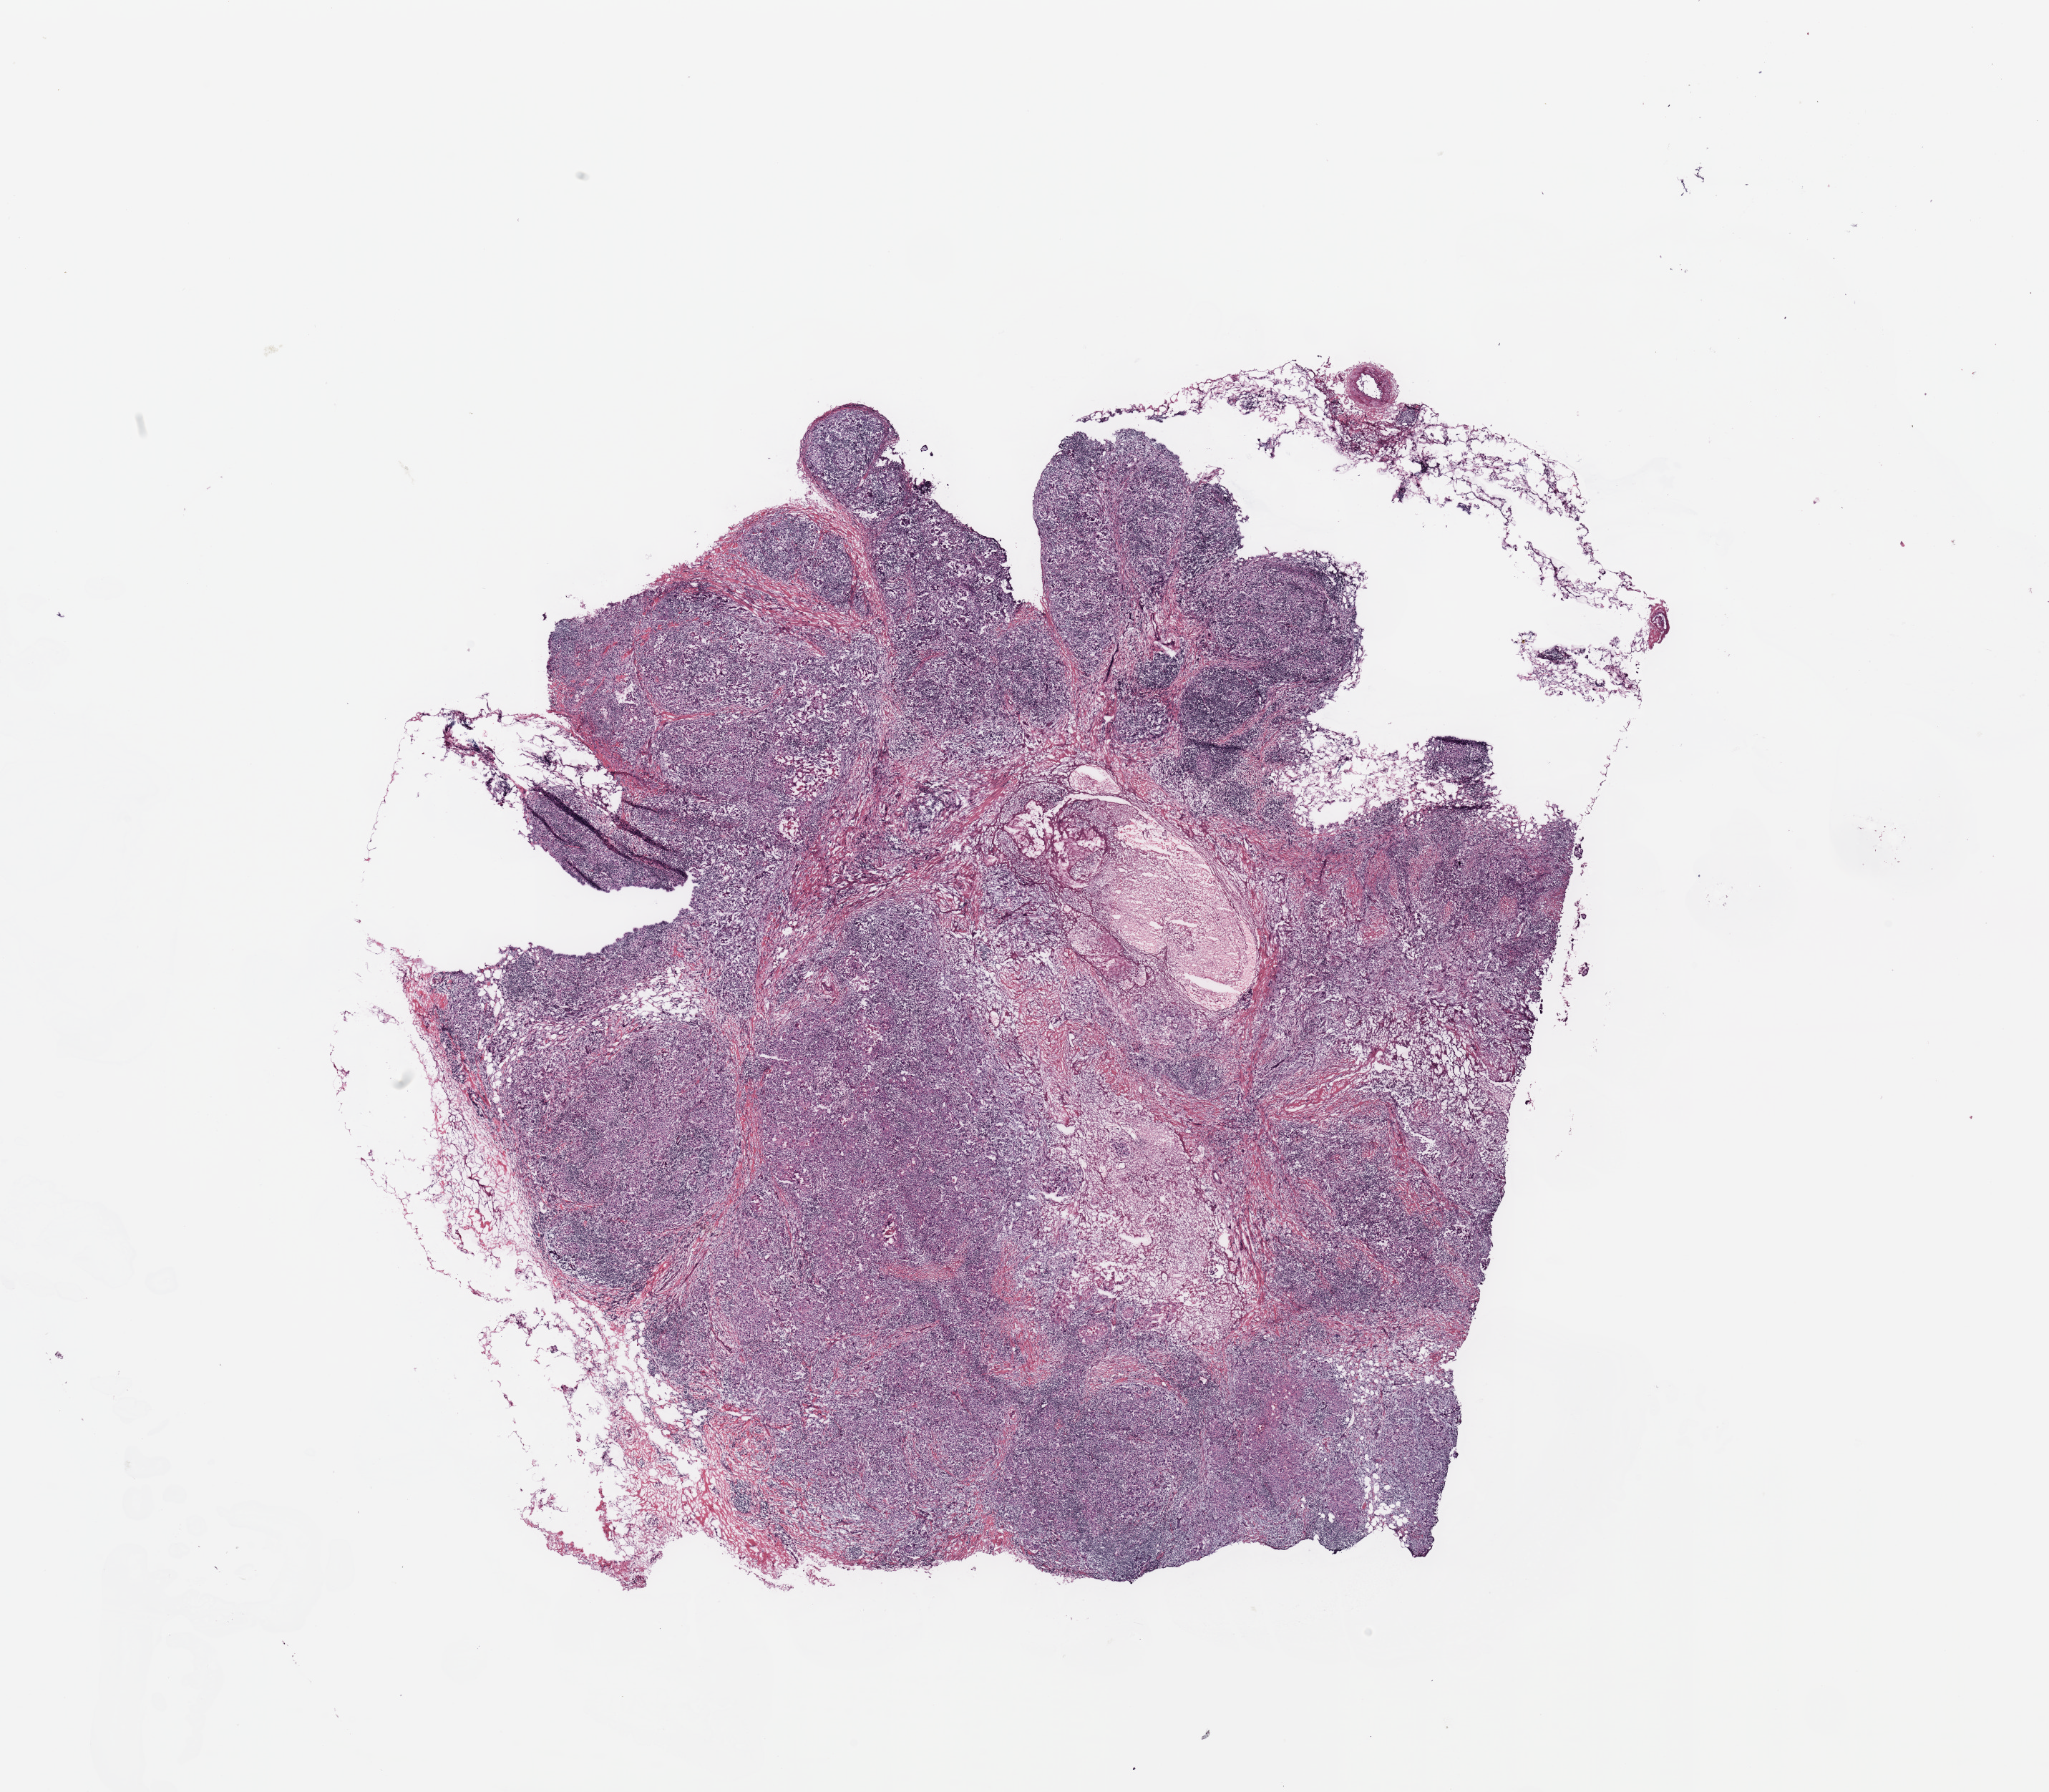
Digitized H&E tissue section (whole slide), shown as a low-resolution overview of the whole scanned area (about 22.6 x 19.8 mm, acquisition: 20x scan); tumour tissue sample, breast. Female, 50 y/o.
* histologic diagnosis: Infiltrating duct carcinoma, NOS
* AJCC pathologic stage: IIA